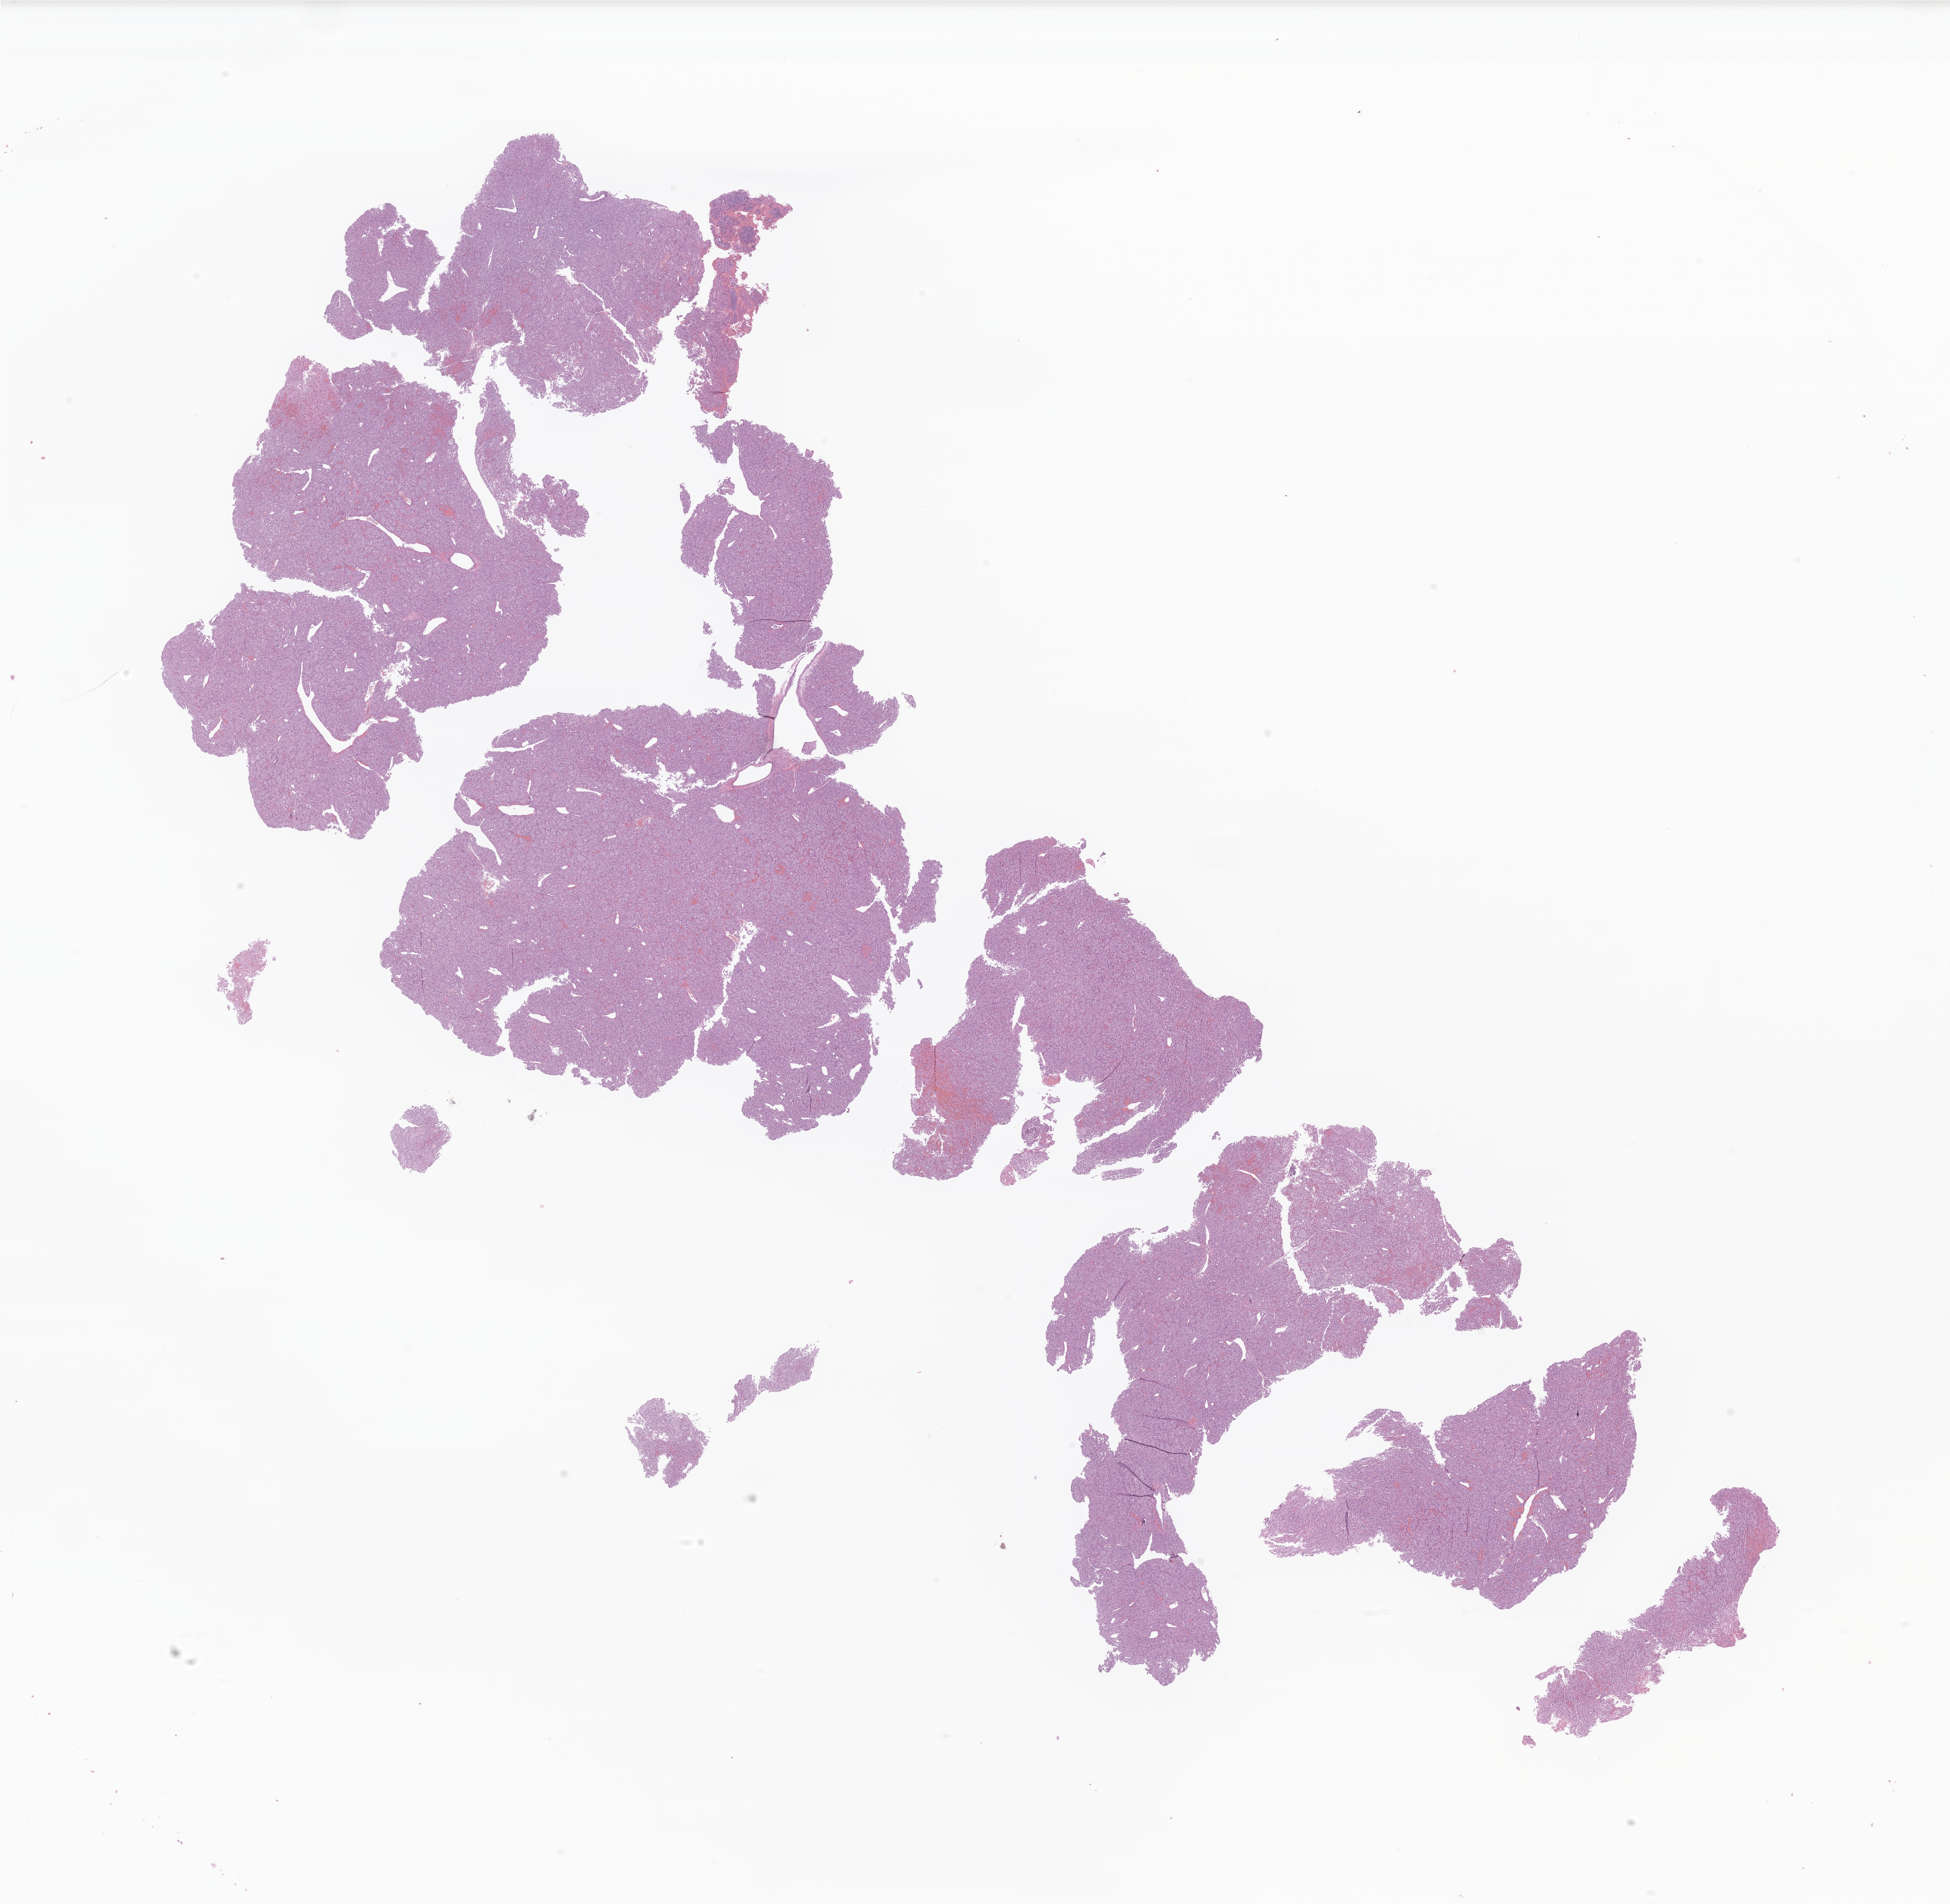
Whole-slide image, hematoxylin and eosin (H&E) stain of tumor tissue from the orbit, low-resolution overview of the scanned area, about 22.6 x 22.1 mm; formalin-fixed paraffin-embedded section. Male patient, age 97 months (8 years 1 month).
Diagnosis: Alveolar soft part sarcoma.